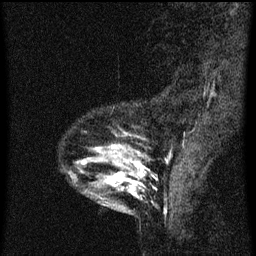
Breast MRI (dynamic contrast-enhanced), one sagittal slice. Slice 14 of 60 in the series (ordered by position). Dynamic contrast-enhanced series, image 2 of 3 at this slice position (ordered by acquisition). 1.5 T. TE 4.2 ms, TR 8 ms. 2 mm slice thickness. 256 × 256 image matrix, field of view 180 × 180 mm. Female patient, age 33 years.
Outlined on this slice (semi-automatic segmentation, software-assisted and operator-edited):
- analysis volume of interest (the breast-tissue region the enhancement analysis was run in; not a lesion): bounding box (x1, y1, x2, y2) in pixels: (69, 132, 146, 213)
- tumour enhancement mask (voxels above the 70 % enhancement threshold inside the analysis volume of interest): (82, 146, 141, 191)